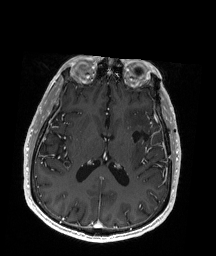
Brain MRI from a brain-tumour surgery series, one axial slice; position 88 of 192 along the scan axis; T1-weighted post-contrast; 1 mm slice thickness; 216 × 256 image matrix, field of view 211 × 250 mm. Case-level facts recorded for this patient, not image findings: histopathology: Oligodendroglioma; WHO grade: 2; IDH mutation: yes.
Structures marked on this image (outlined manually by an expert reader):
- previous resection cavity: bounding box <132,124,163,140> (left, top, right, bottom; pixels)